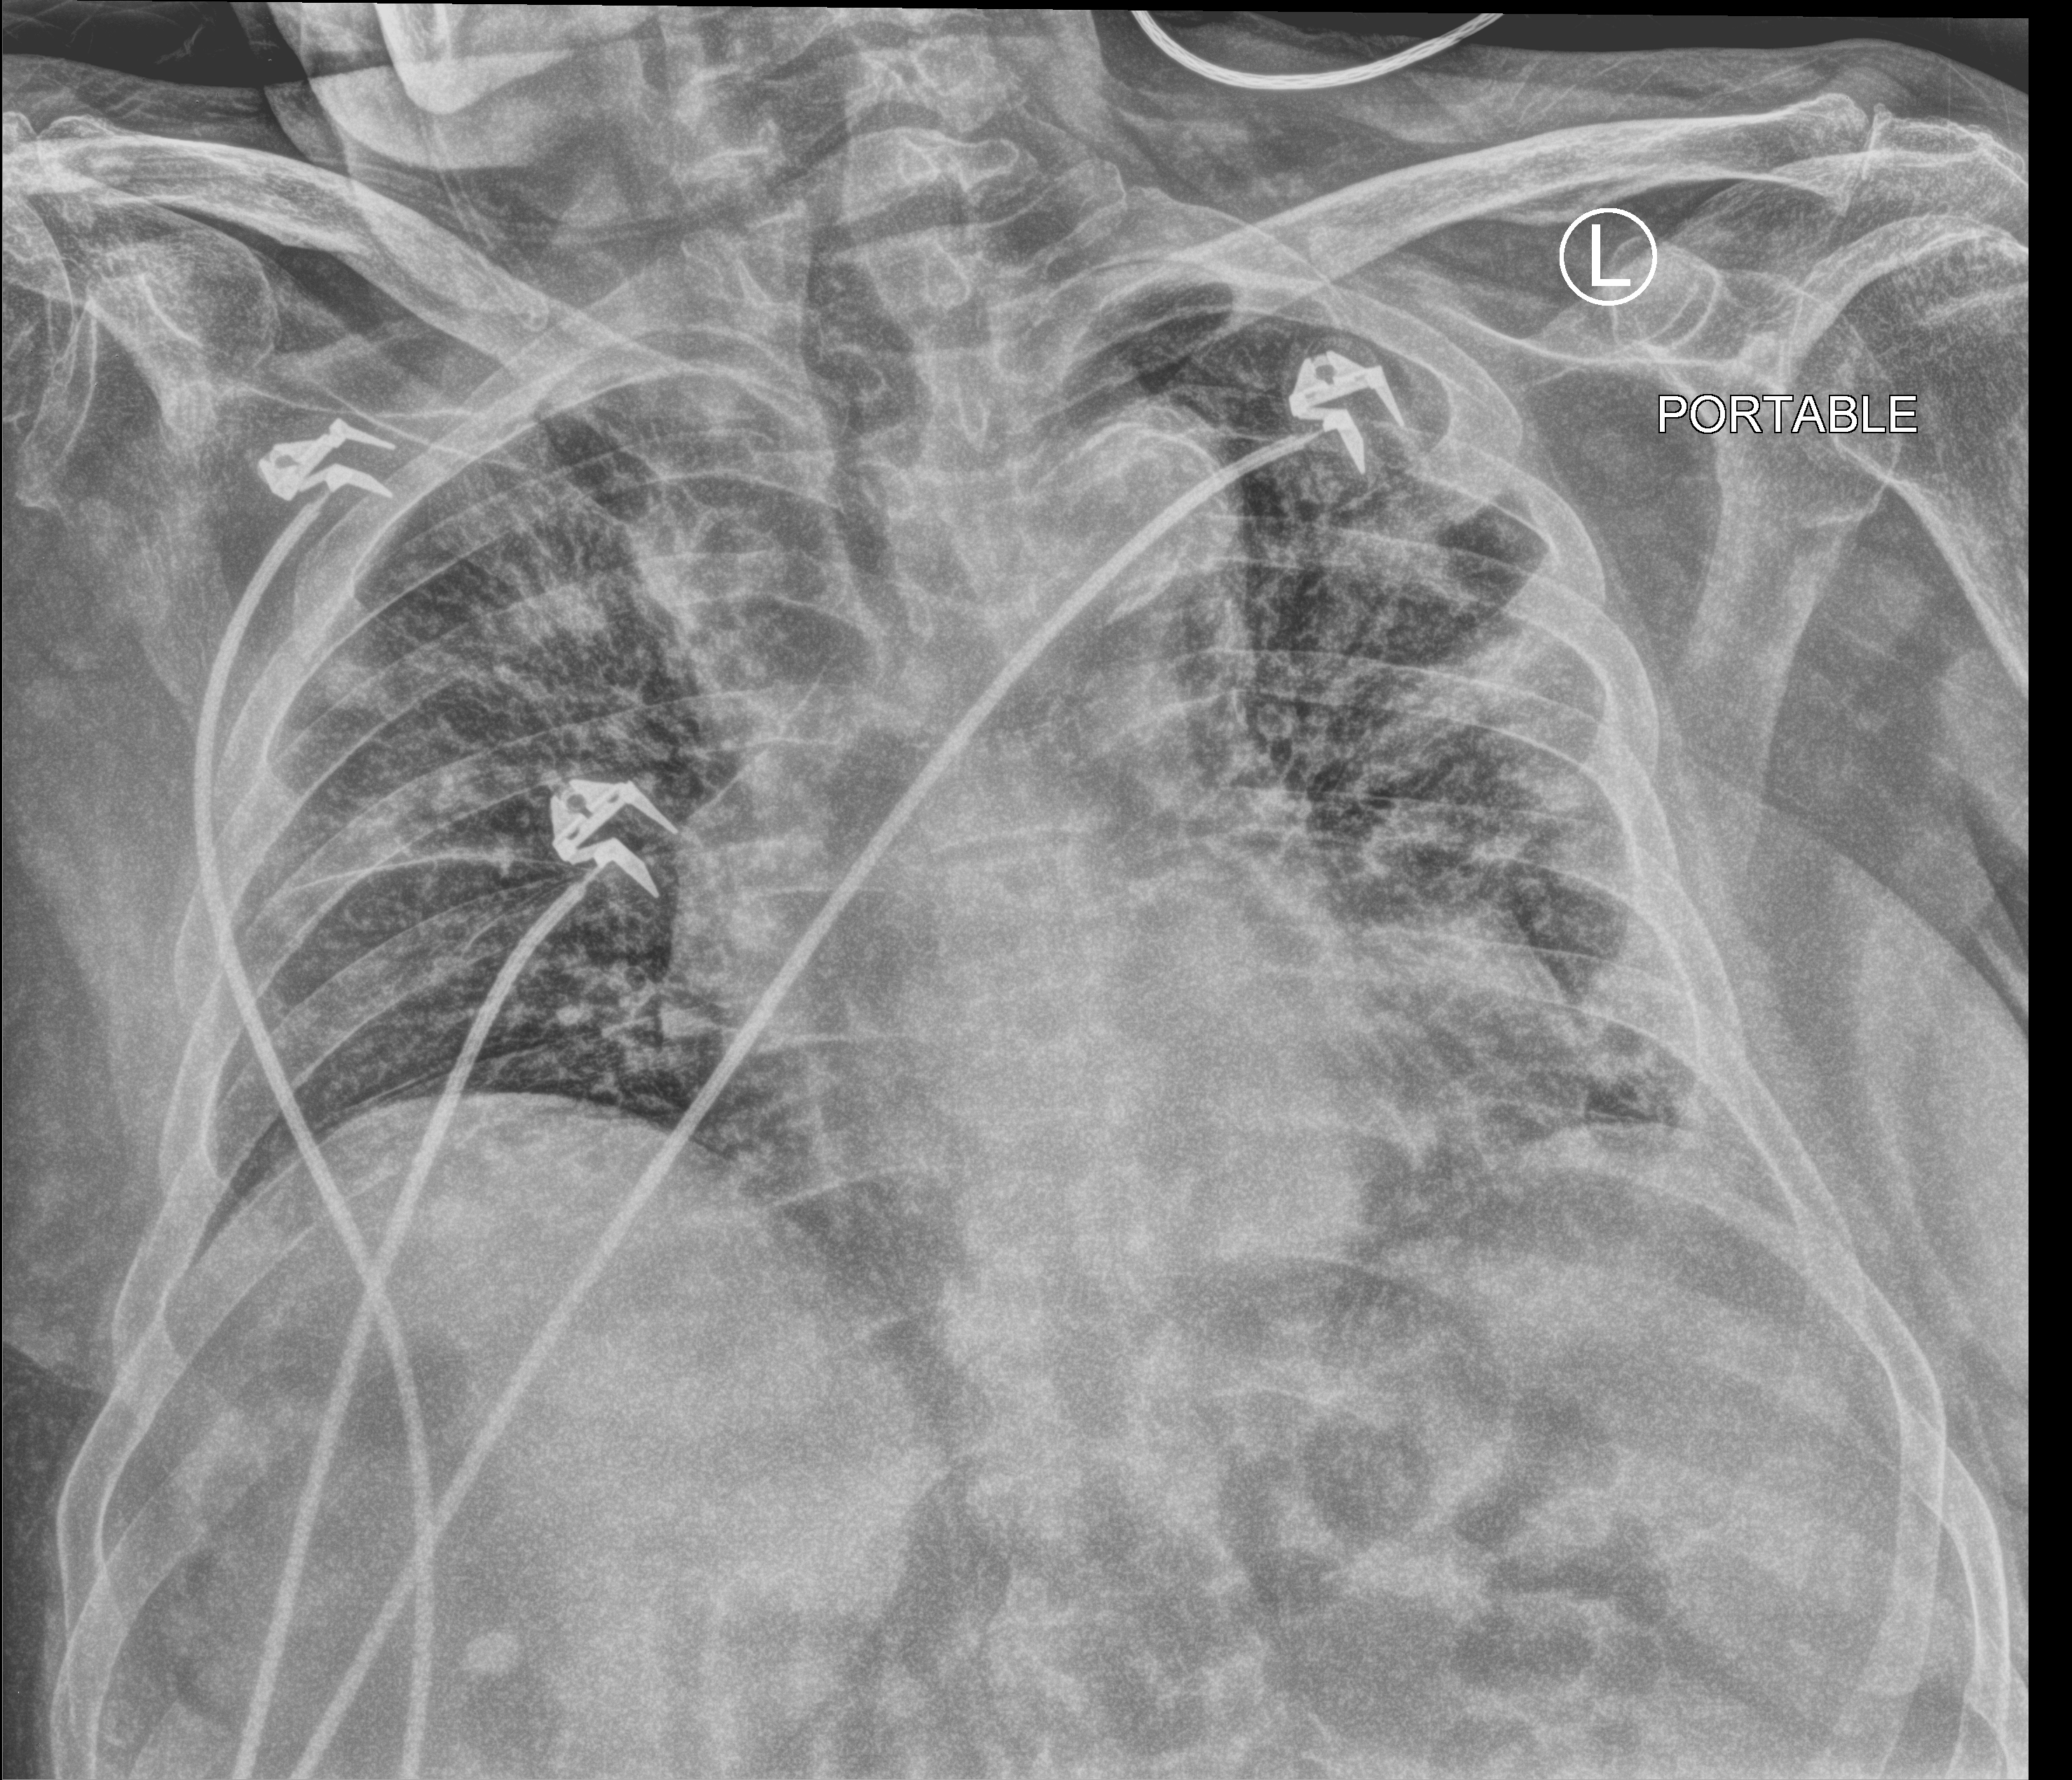
Chest X-ray (portable), anteroposterior (AP) projection. Patient hospitalised with COVID-19; male, aged 75–90 years.
Admission-level facts for this patient (not findings on this image; timing relative to this image not recorded): admitted to intensive care during this hospital stay: no; mechanically ventilated during this hospital stay: no.